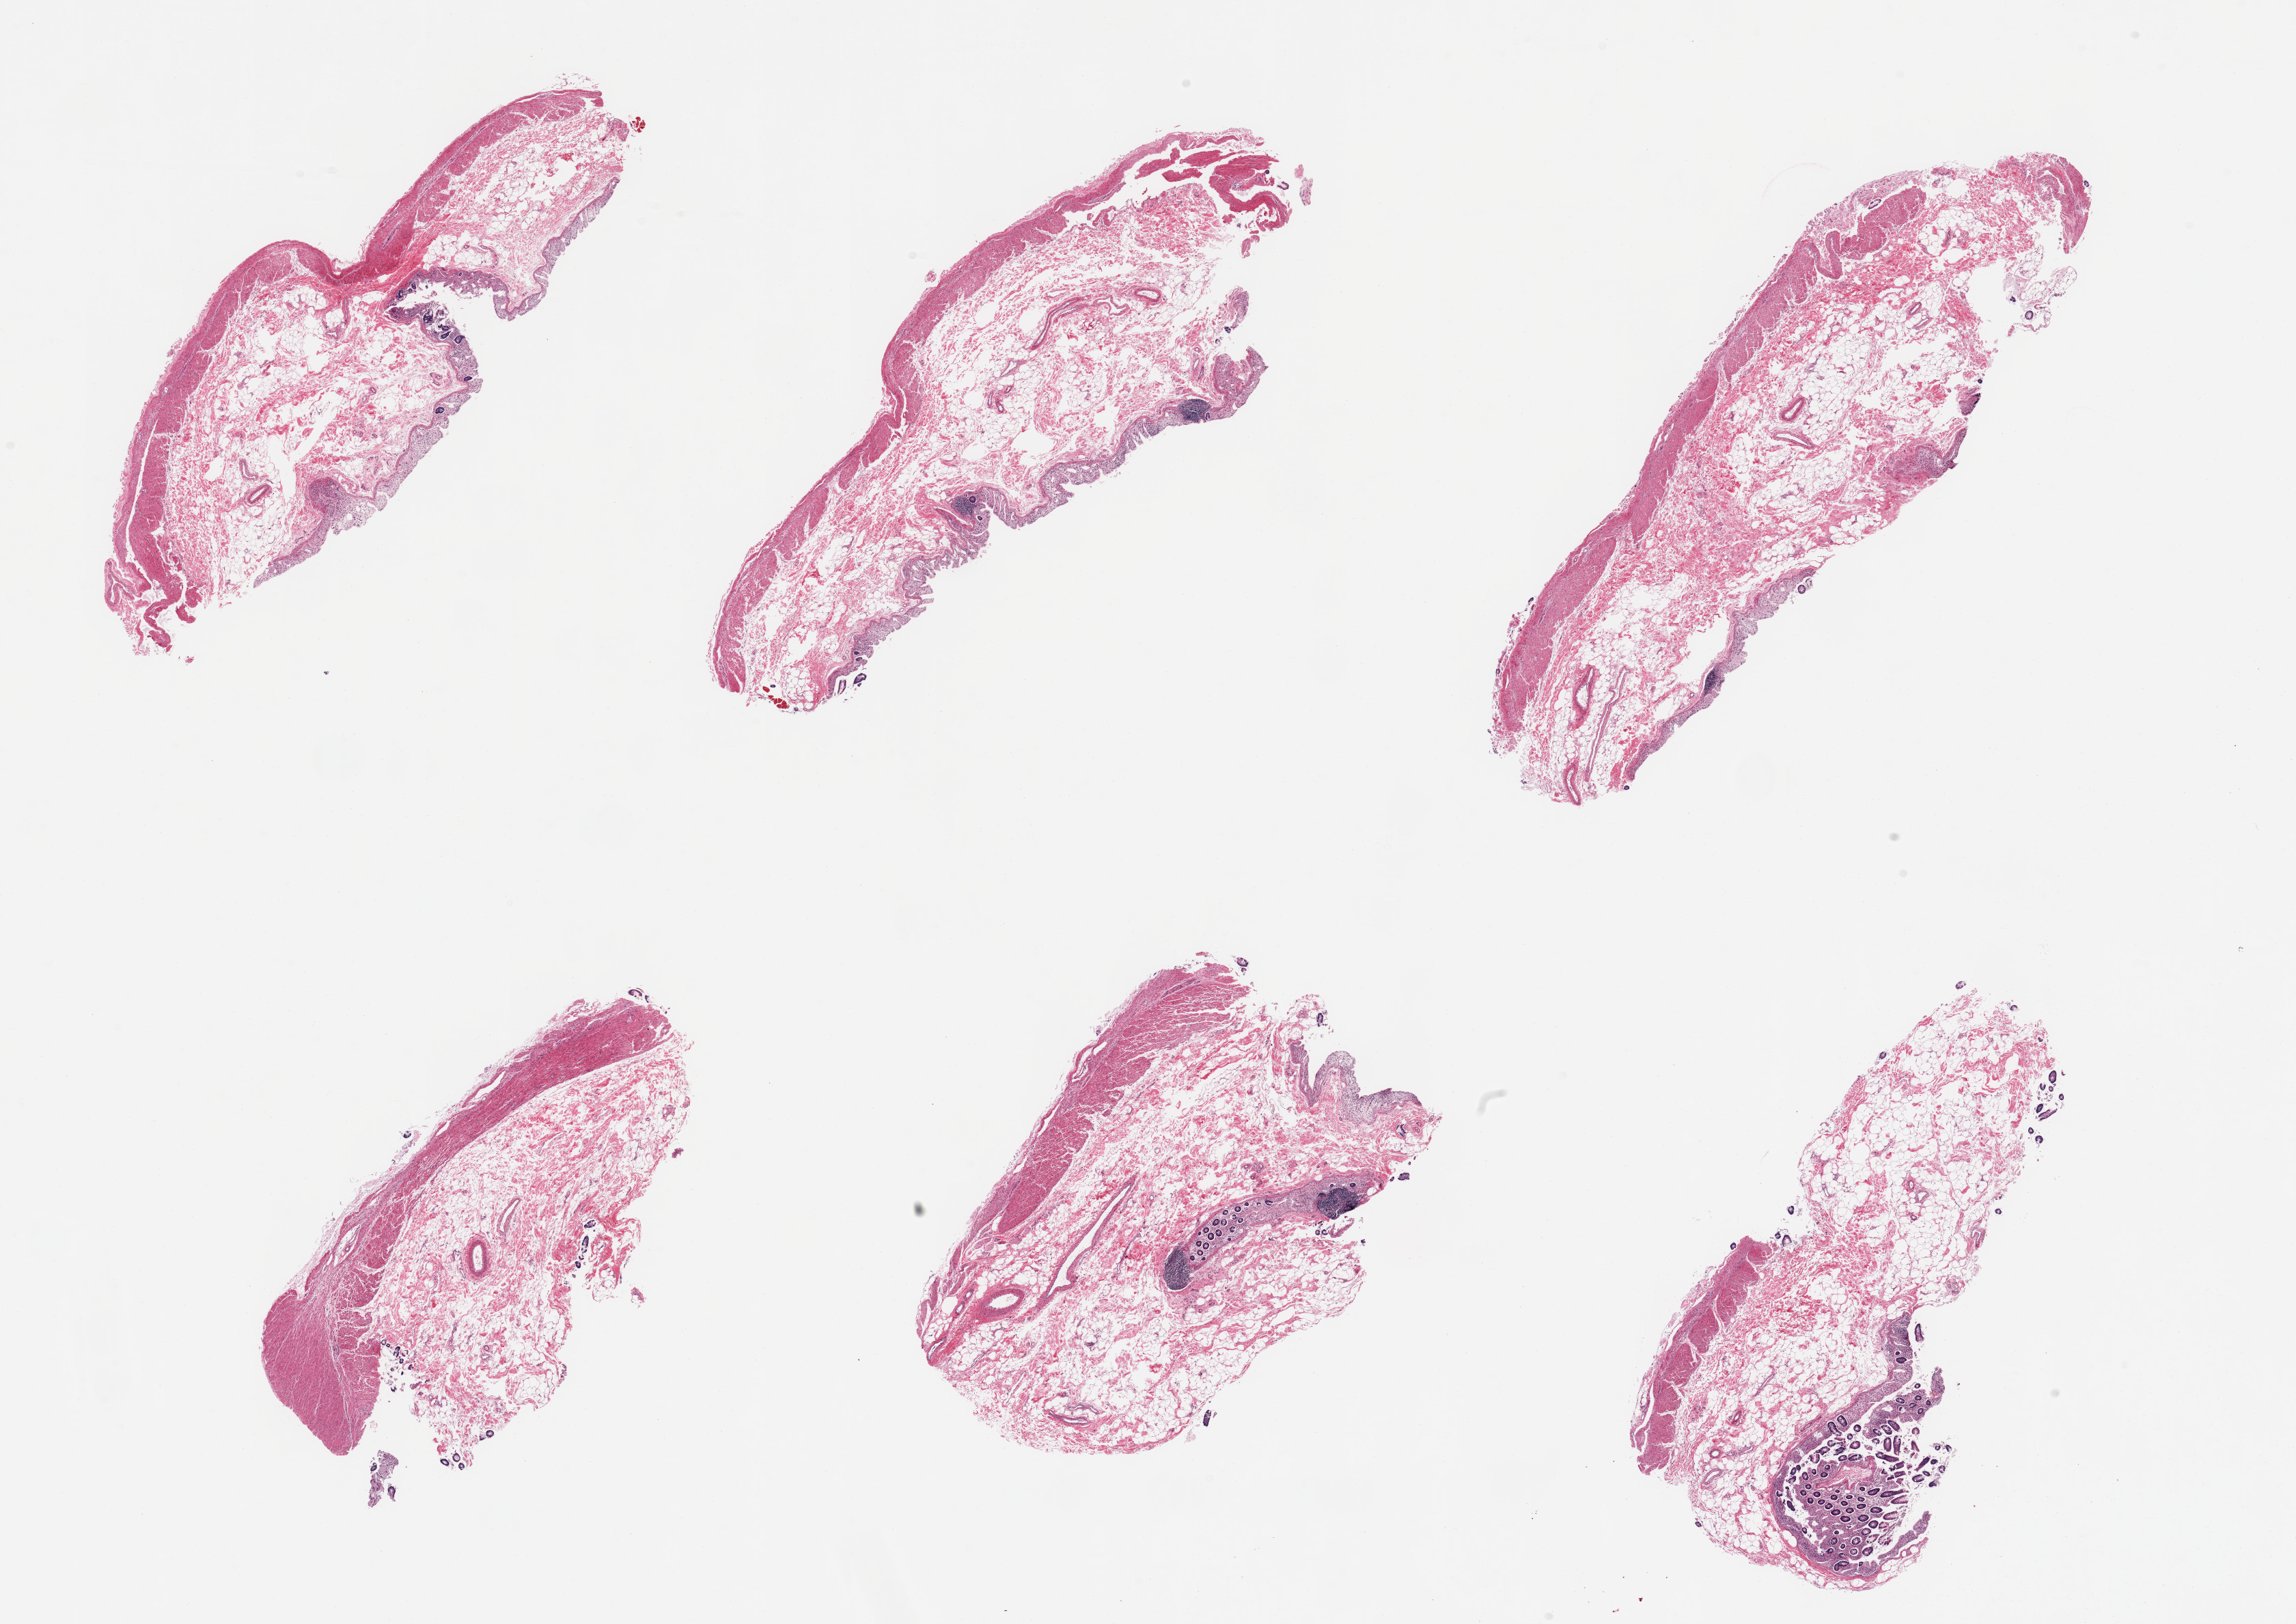
Whole-slide image, H&E stain, brightfield, whole scanned area (about 26.6 x 18.8 mm, acquisition: 20x scan) shown as a low-resolution overview, PAXgene-fixed, paraffin-embedded tissue, sampled site (target tissue): transverse colon, tissue donor sample. Male donor.
* review note (as recorded): 6 pieces; advanced autolysis of mucosa and preserved muscularis